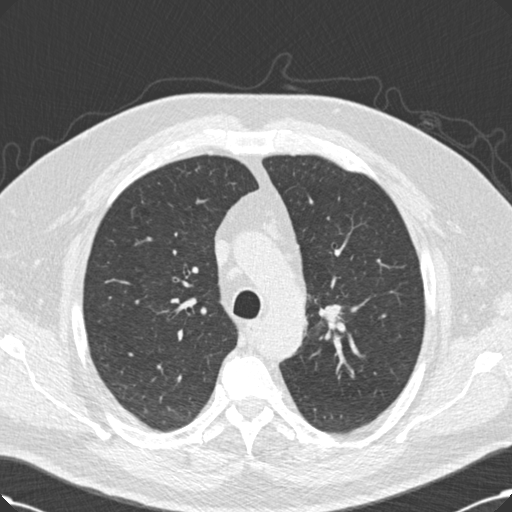
Chest CT (low-dose screening protocol), one axial image, third screening round (two years after baseline), lung window (W 1500 / L -600 HU), 2 mm slice thickness, standard (soft-tissue) reconstruction kernel (B30f), slice 55 of 214 in the series. Male, age 60 years at enrolment.
Lesion marked by an expert reader, bounding box (x1, y1, x2, y2) in pixels: (318, 300, 350, 333). Screening reader's record for this exam (one nodule recorded; not confirmed to be the boxed lesion): non-calcified nodule or mass ≥4 mm, left upper lobe, 20 × 20 mm, smooth margins, soft tissue attenuation, pre-existing on the prior screen: no. Official screen result: positive, other. Later outcome: lung cancer diagnosed 53 days after this screen — squamous cell carcinoma, NOS, right upper lobe, 27 mm at pathology.